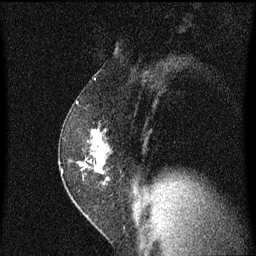
Breast MRI (dynamic contrast-enhanced), one sagittal slice. Position 38 of 60 along the scan axis. Dynamic contrast-enhanced series, image 2 of 3 at this slice position (ordered by acquisition). 1.5 T. TE 4.2 ms, TR 8.4 ms. 2 mm slice thickness. 256 × 256 image matrix, field of view 200 × 200 mm. Female patient, age 52 years. Case-level facts recorded for this patient, not image findings: setting: breast cancer imaged before/during neoadjuvant chemotherapy; receptor status: HER2-positive.
Annotated regions visible in this slice (semi-automatic segmentation, software-assisted and operator-edited):
- analysis volume of interest (the breast-tissue region the enhancement analysis was run in; not a lesion): bounding box [x1, y1, x2, y2] px = [60, 124, 115, 191]
- tumour enhancement mask (voxels above the 70 % enhancement threshold inside the analysis volume of interest): [90, 130, 104, 171]